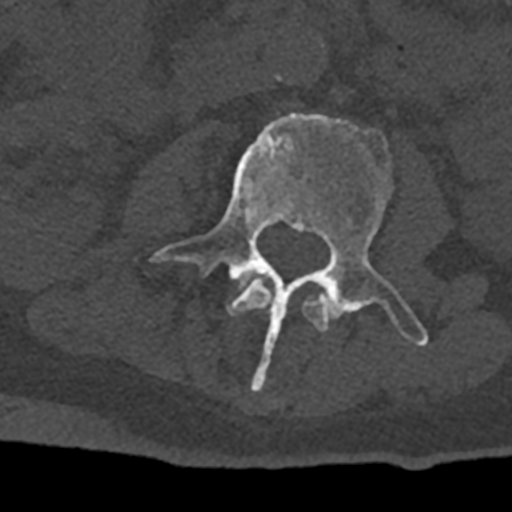
CT including the spine, one axial slice; position 328 of 797 along the scan axis; 120 kVp; bone window (W 1800 / L 400 HU); 0.5 mm slice thickness; 512 × 512 image matrix, field of view 160 × 160 mm. Patient: male, 74 years. From the clinical record (not read from this slice): primary cancer: renal.
Structures marked on this image (semi-automatically segmented with operator editing):
- L2 vertebra: bounding box [x1, y1, x2, y2] px = [228, 280, 329, 332]
- L3 vertebra: [150, 113, 428, 392]